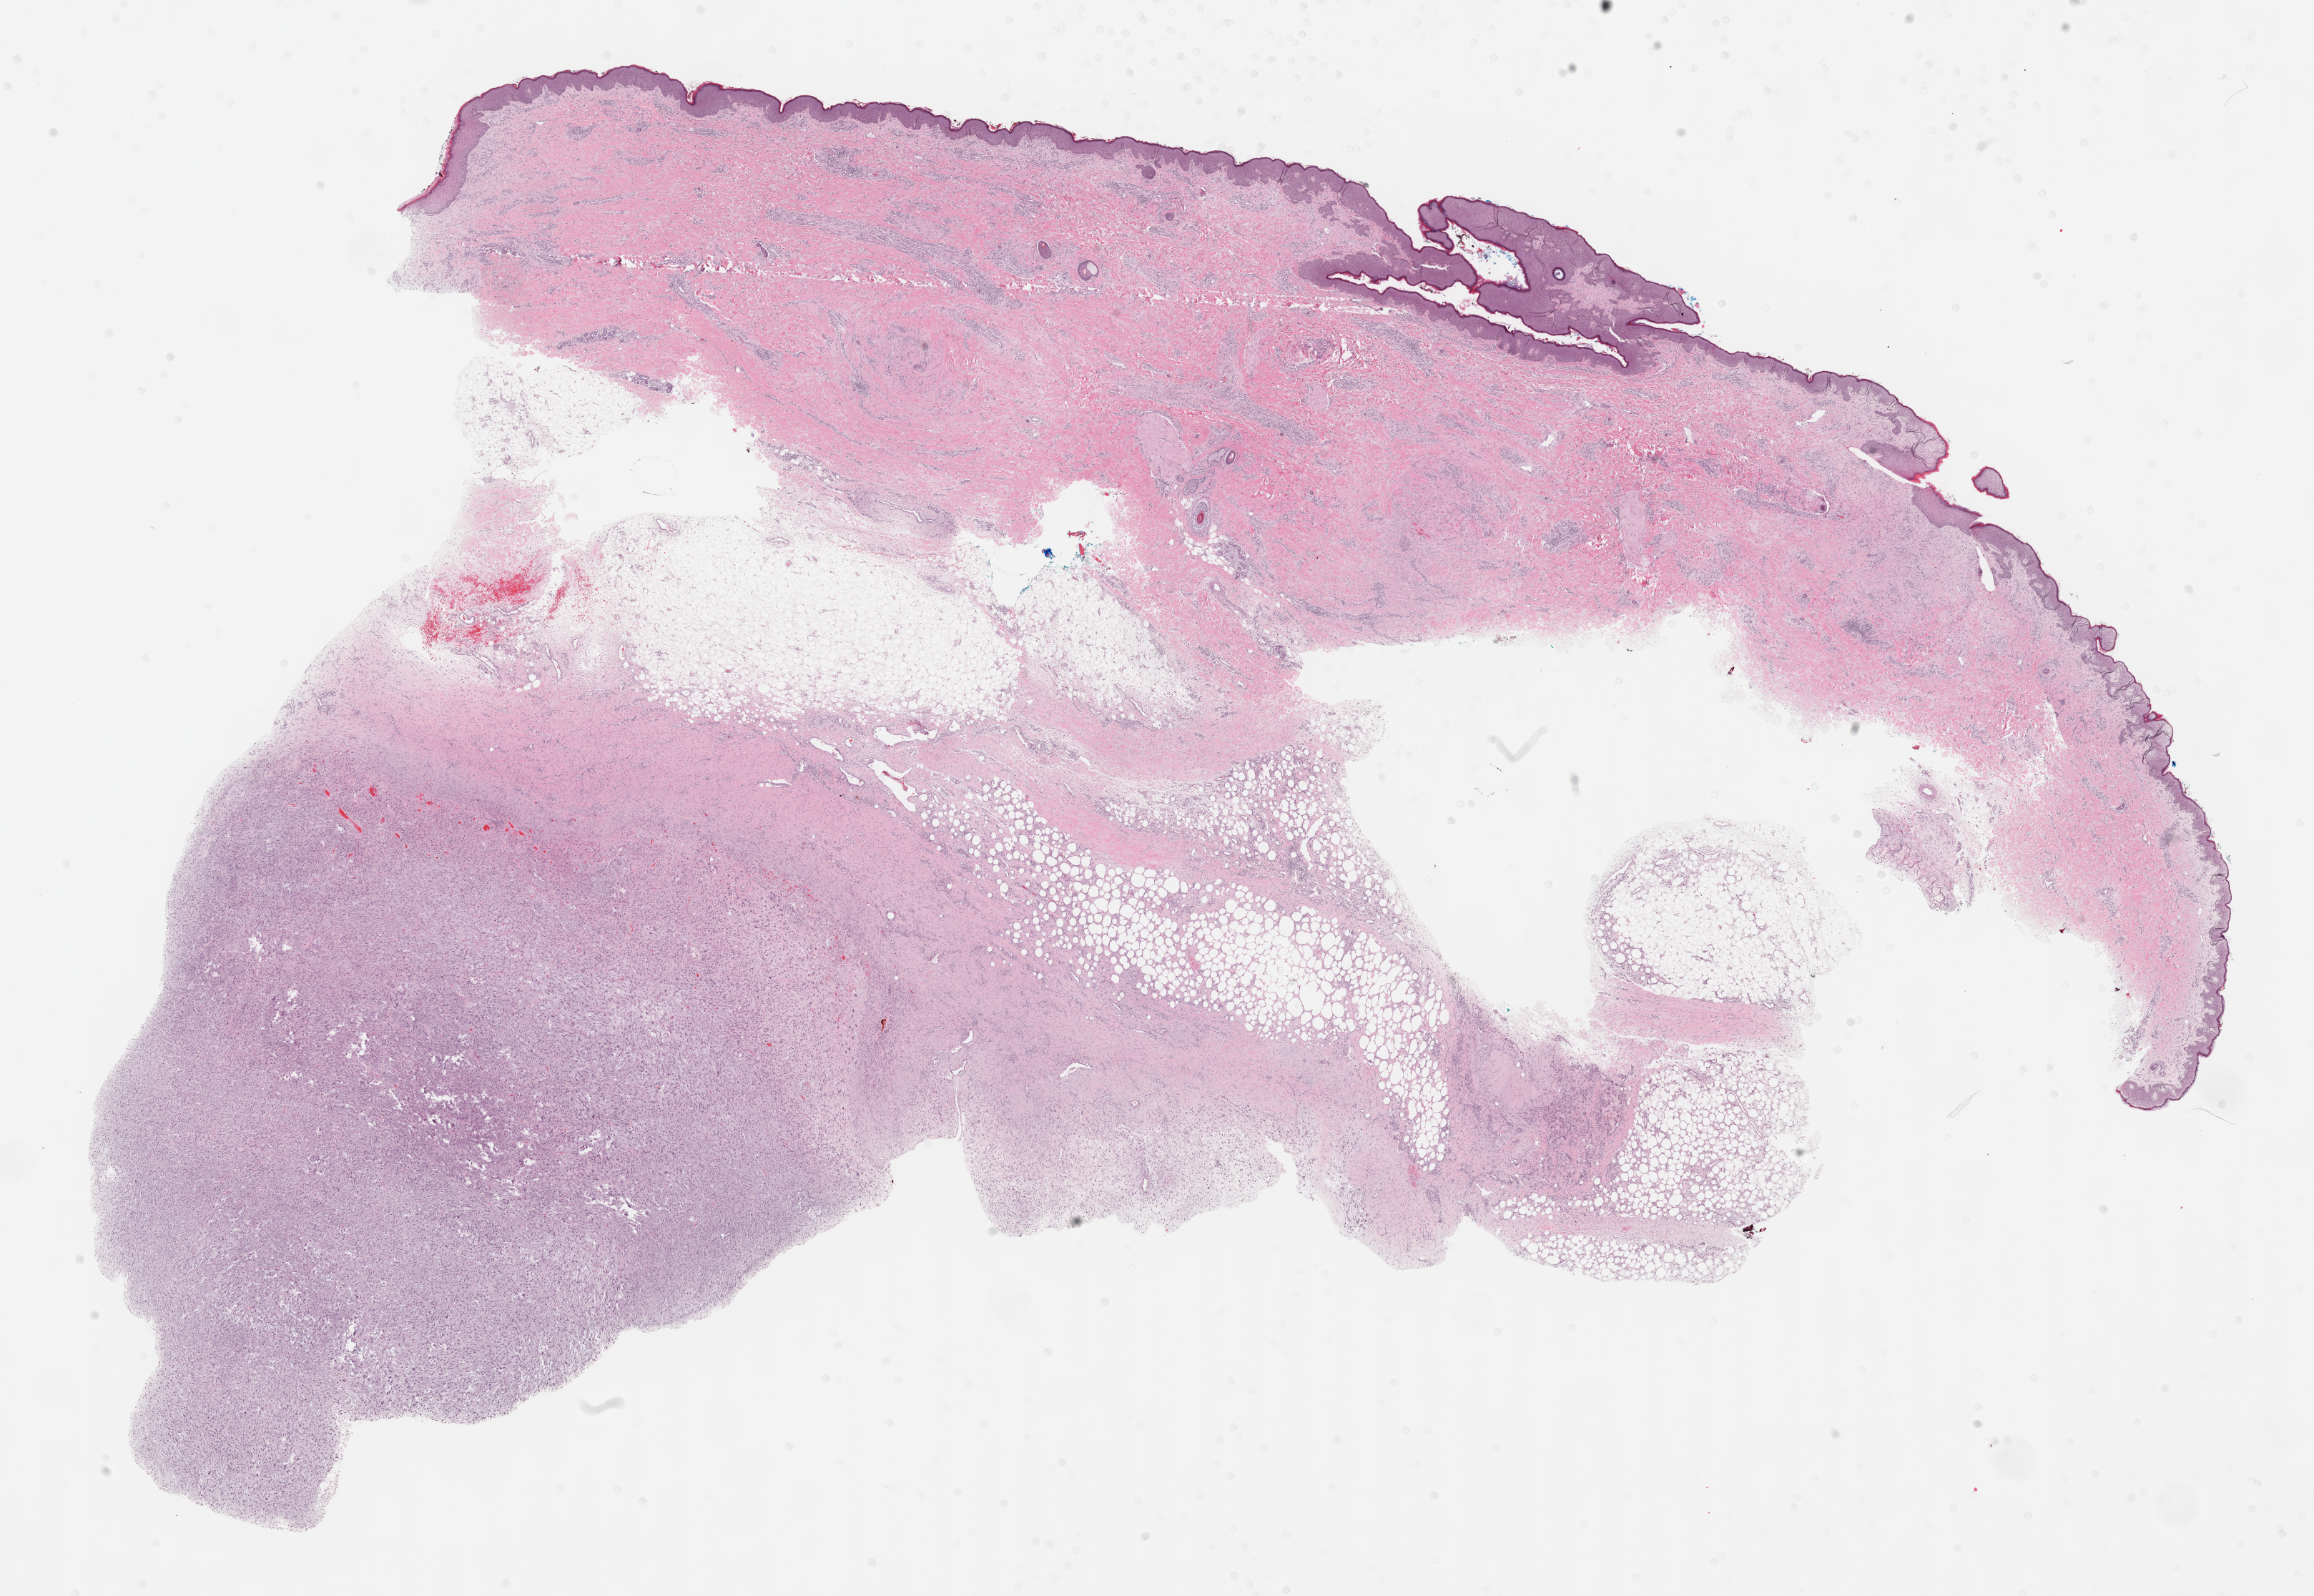
Whole-slide histology image, Hematoxylin and eosin (H&E) stained, a low-resolution overview of the entire scanned area, about 26.2 x 18.1 mm (acquisition: 40x scan); FFPE section; primary tumour sample from the connective, subcutaneous and other soft tissues. Female, age 31 years at initial diagnosis.
- pathologic diagnosis: Fibromyxosarcoma (connective, subcutaneous and other soft tissues of lower limb and hip)